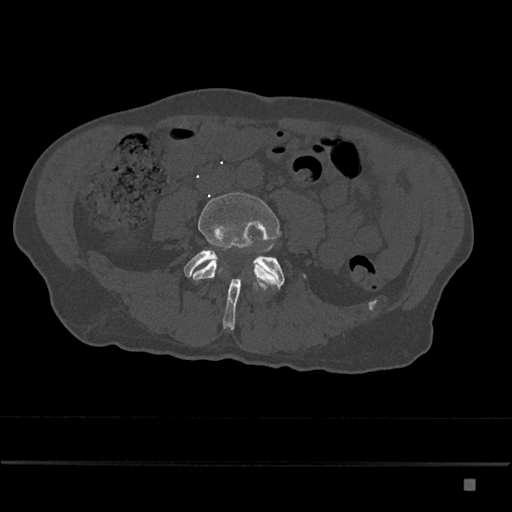
CT including the spine, one axial slice. Slice 311 of 797 in the series (ordered by position). Bone window (W 1800 / L 400 HU). 512 × 512 image matrix, field of view 390 × 390 mm. Male patient, age 72 years. Case-level facts recorded for this patient, not image findings: primary cancer: prostate.
Annotated regions visible in this slice (semi-automatically segmented with operator editing):
- L4 vertebra: bounding box [x1, y1, x2, y2] px = [190, 192, 281, 287]
- L5 vertebra: [184, 250, 305, 330]